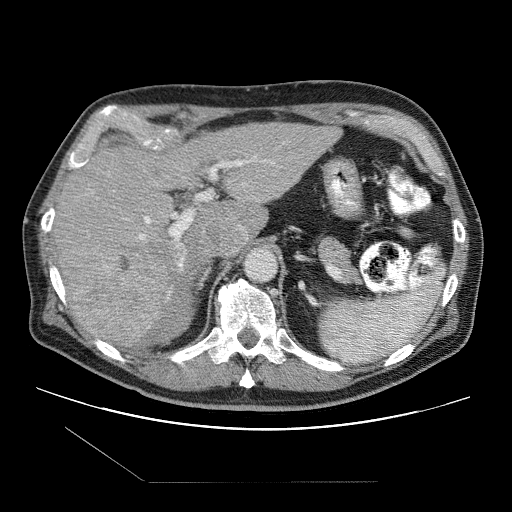
Contrast-enhanced abdominal CT (liver protocol), one axial slice; position 66 of 109 along the scan axis; 120 kVp; one of 2 acquisitions stored at this slice position; soft-tissue window (W 400 / L 40 HU); 2.5 mm slice thickness; 512 × 512 image matrix, field of view 400 × 400 mm. From the clinical record (not read from this slice): diagnosis: hepatocellular carcinoma (patient treated with transarterial chemoembolisation; whether this scan precedes or follows treatment is not stated here); TNM stage (as recorded): Stage-IIIB; Child-Pugh class: A; tumour differentiation: well differentiated; tumour nodularity: multinodular.
Outlined on this slice (semi-automatically segmented with operator editing):
- abdominal aorta: bounding box (x1, y1, x2, y2) in pixels: (246, 248, 278, 281)
- liver parenchyma outside the tumour (the mass and vessels are separate outlines, so this box may not span the whole liver): (52, 122, 340, 346)
- mass: (57, 238, 169, 346)
- liver vessels: (139, 160, 250, 328)